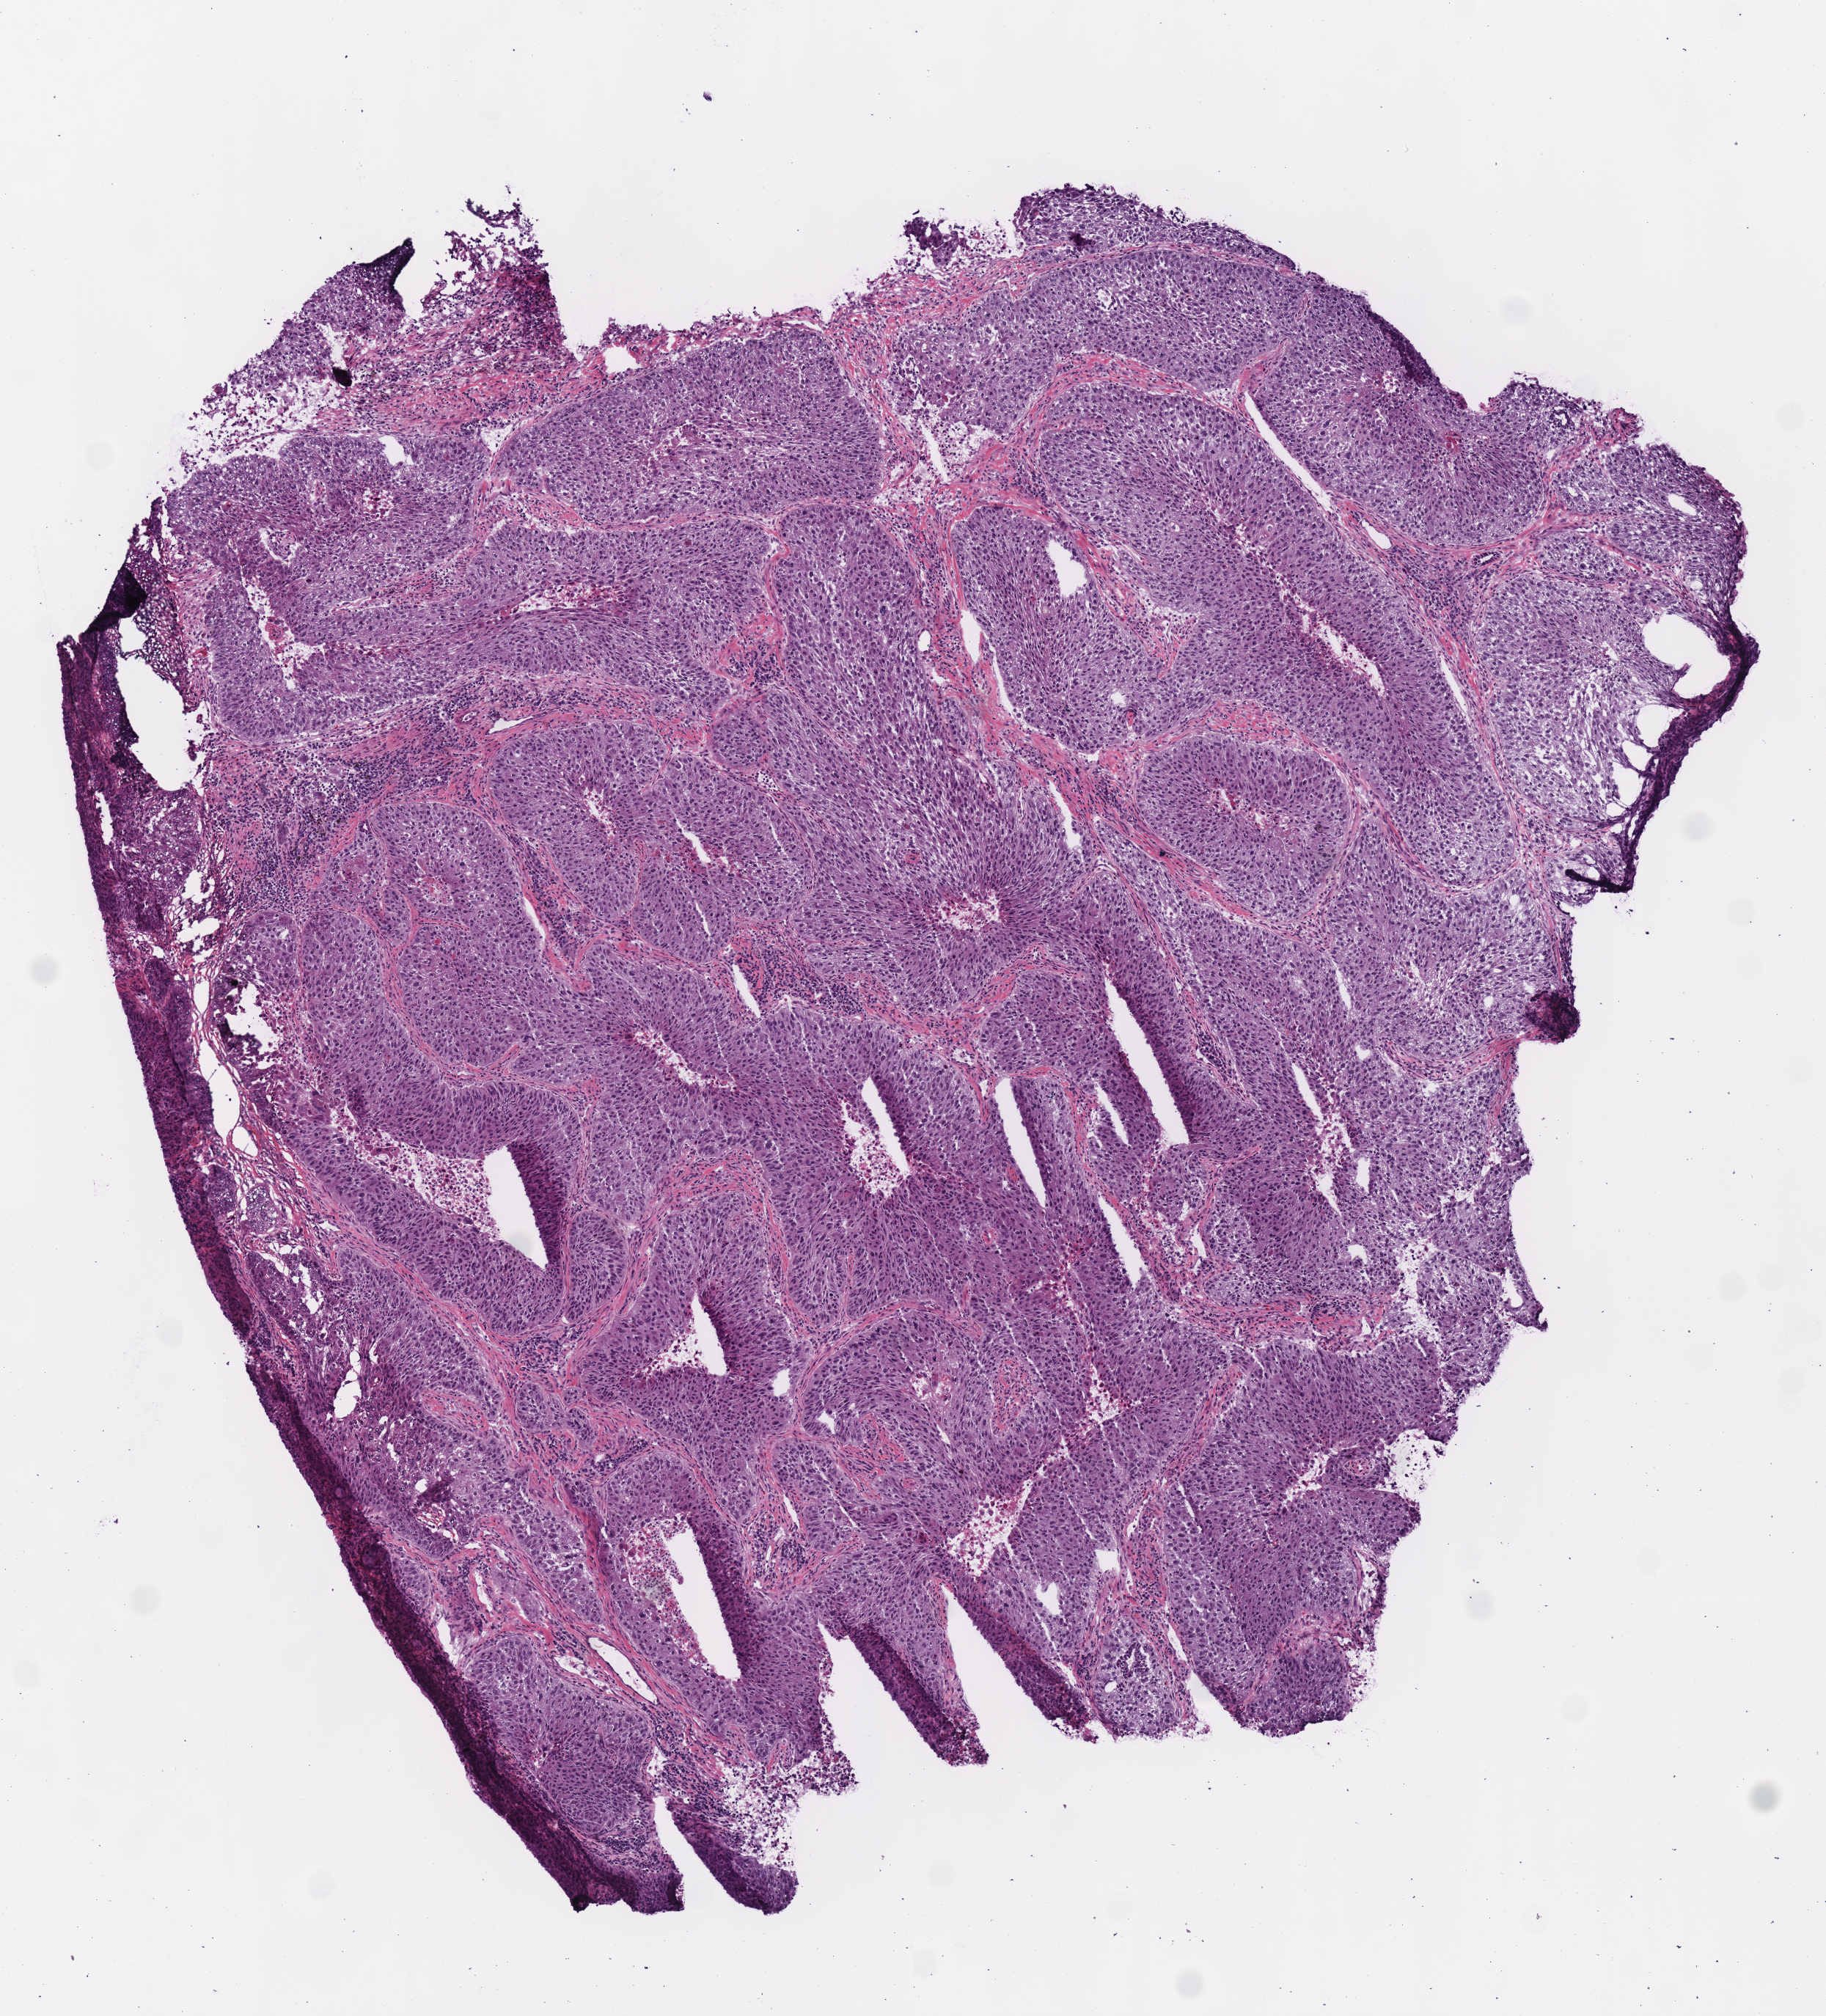
Whole-slide histology image, H&E, shown as a low-resolution overview of the whole scanned area (about 4.9 x 5.4 mm, slide scanned at 40x), frozen section from the bottom of the tissue portion, sample: primary tumour, lung. Female, age 57 years at initial diagnosis. Composition of this section per pathologist review: tumour cells 95%, tumour nuclei 88%, normal cells 0%, stromal cells 3%, necrosis 2%. Infiltration values recorded for this section: lymphocyte infiltration 8%.
Diagnosis: Squamous cell carcinoma, NOS. TNM: T2 N2 M0. AJCC pathologic stage: IIIA.